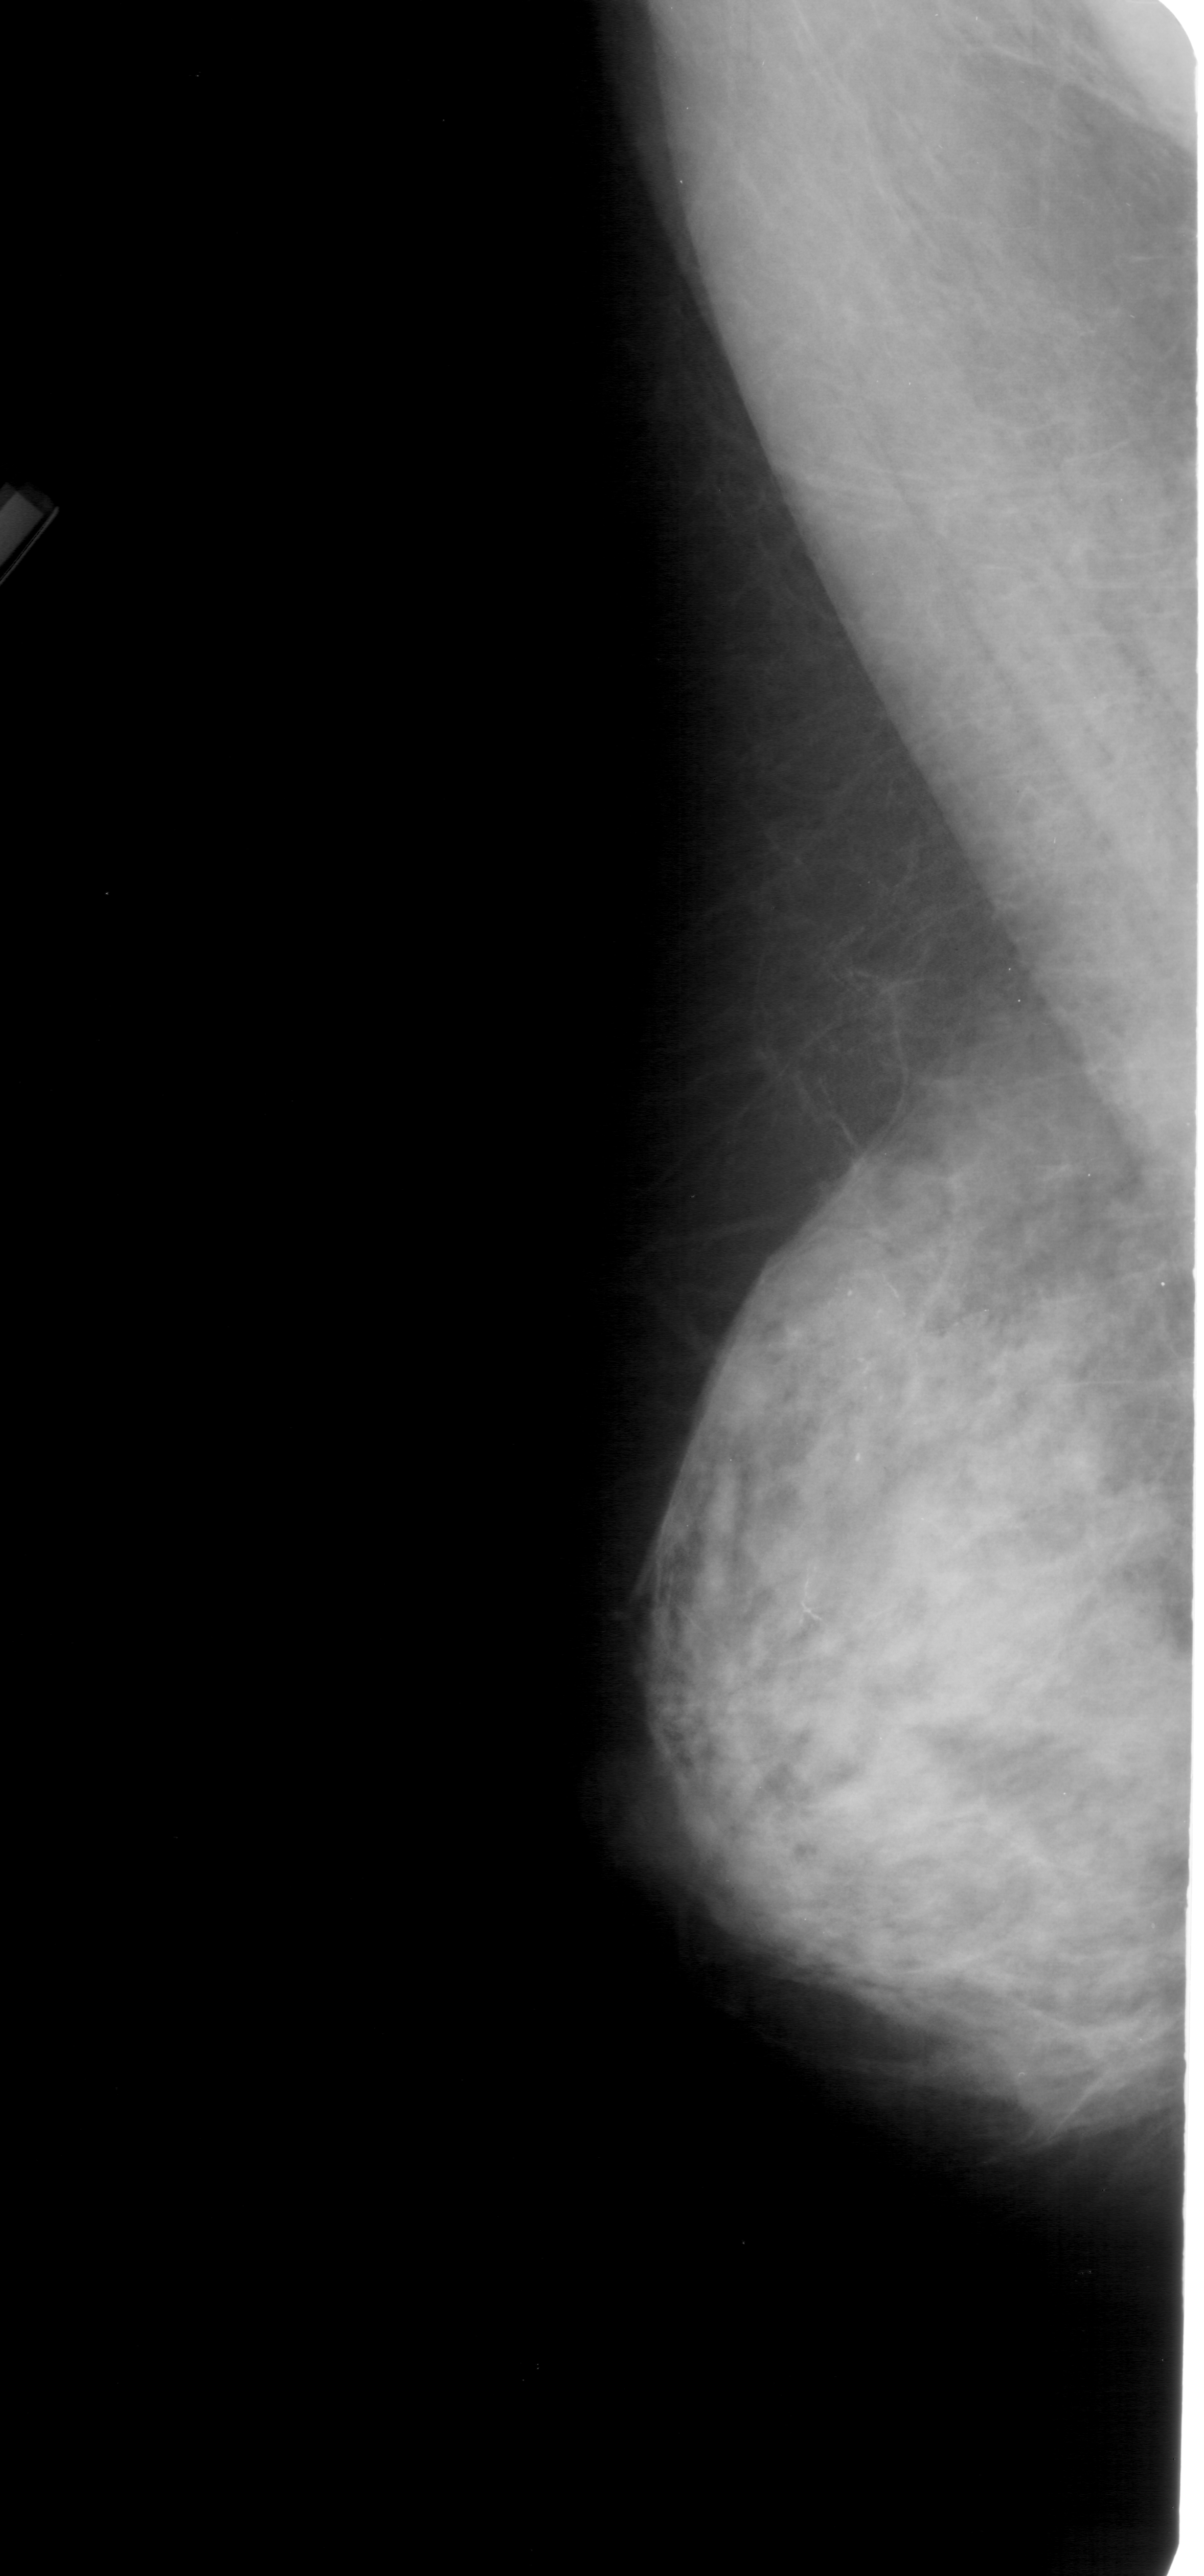
Digitized screen-film mammogram. Left breast. MLO view. BI-RADS breast density category 4 (scale 1–4). 1204 × 2576 image matrix.
Marked abnormalities (boxes around the expert regions of interest):
- calcifications, morphology pleomorphic, distribution segmental; BI-RADS assessment category 4; subtlety rating 3 on a 1 (subtle) to 5 (obvious) scale; pathology (as recorded): malignant: bounding box <692,1241,965,1663> (left, top, right, bottom; pixels)